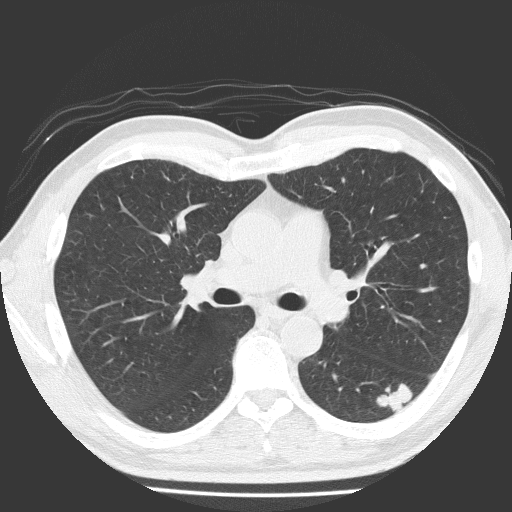
Low-dose screening chest CT, one axial slice; position 110 of 184 along the scan axis; reconstruction kernel FC51; lung window (W 1500 / L -600 HU); 2 mm slice thickness; 512 × 512 image matrix.
Structures marked on this image (manually delineated by an expert):
- lesion 1 (tumor, lower lobe of left lung): bounding box <376,383,413,412> (left, top, right, bottom; pixels)